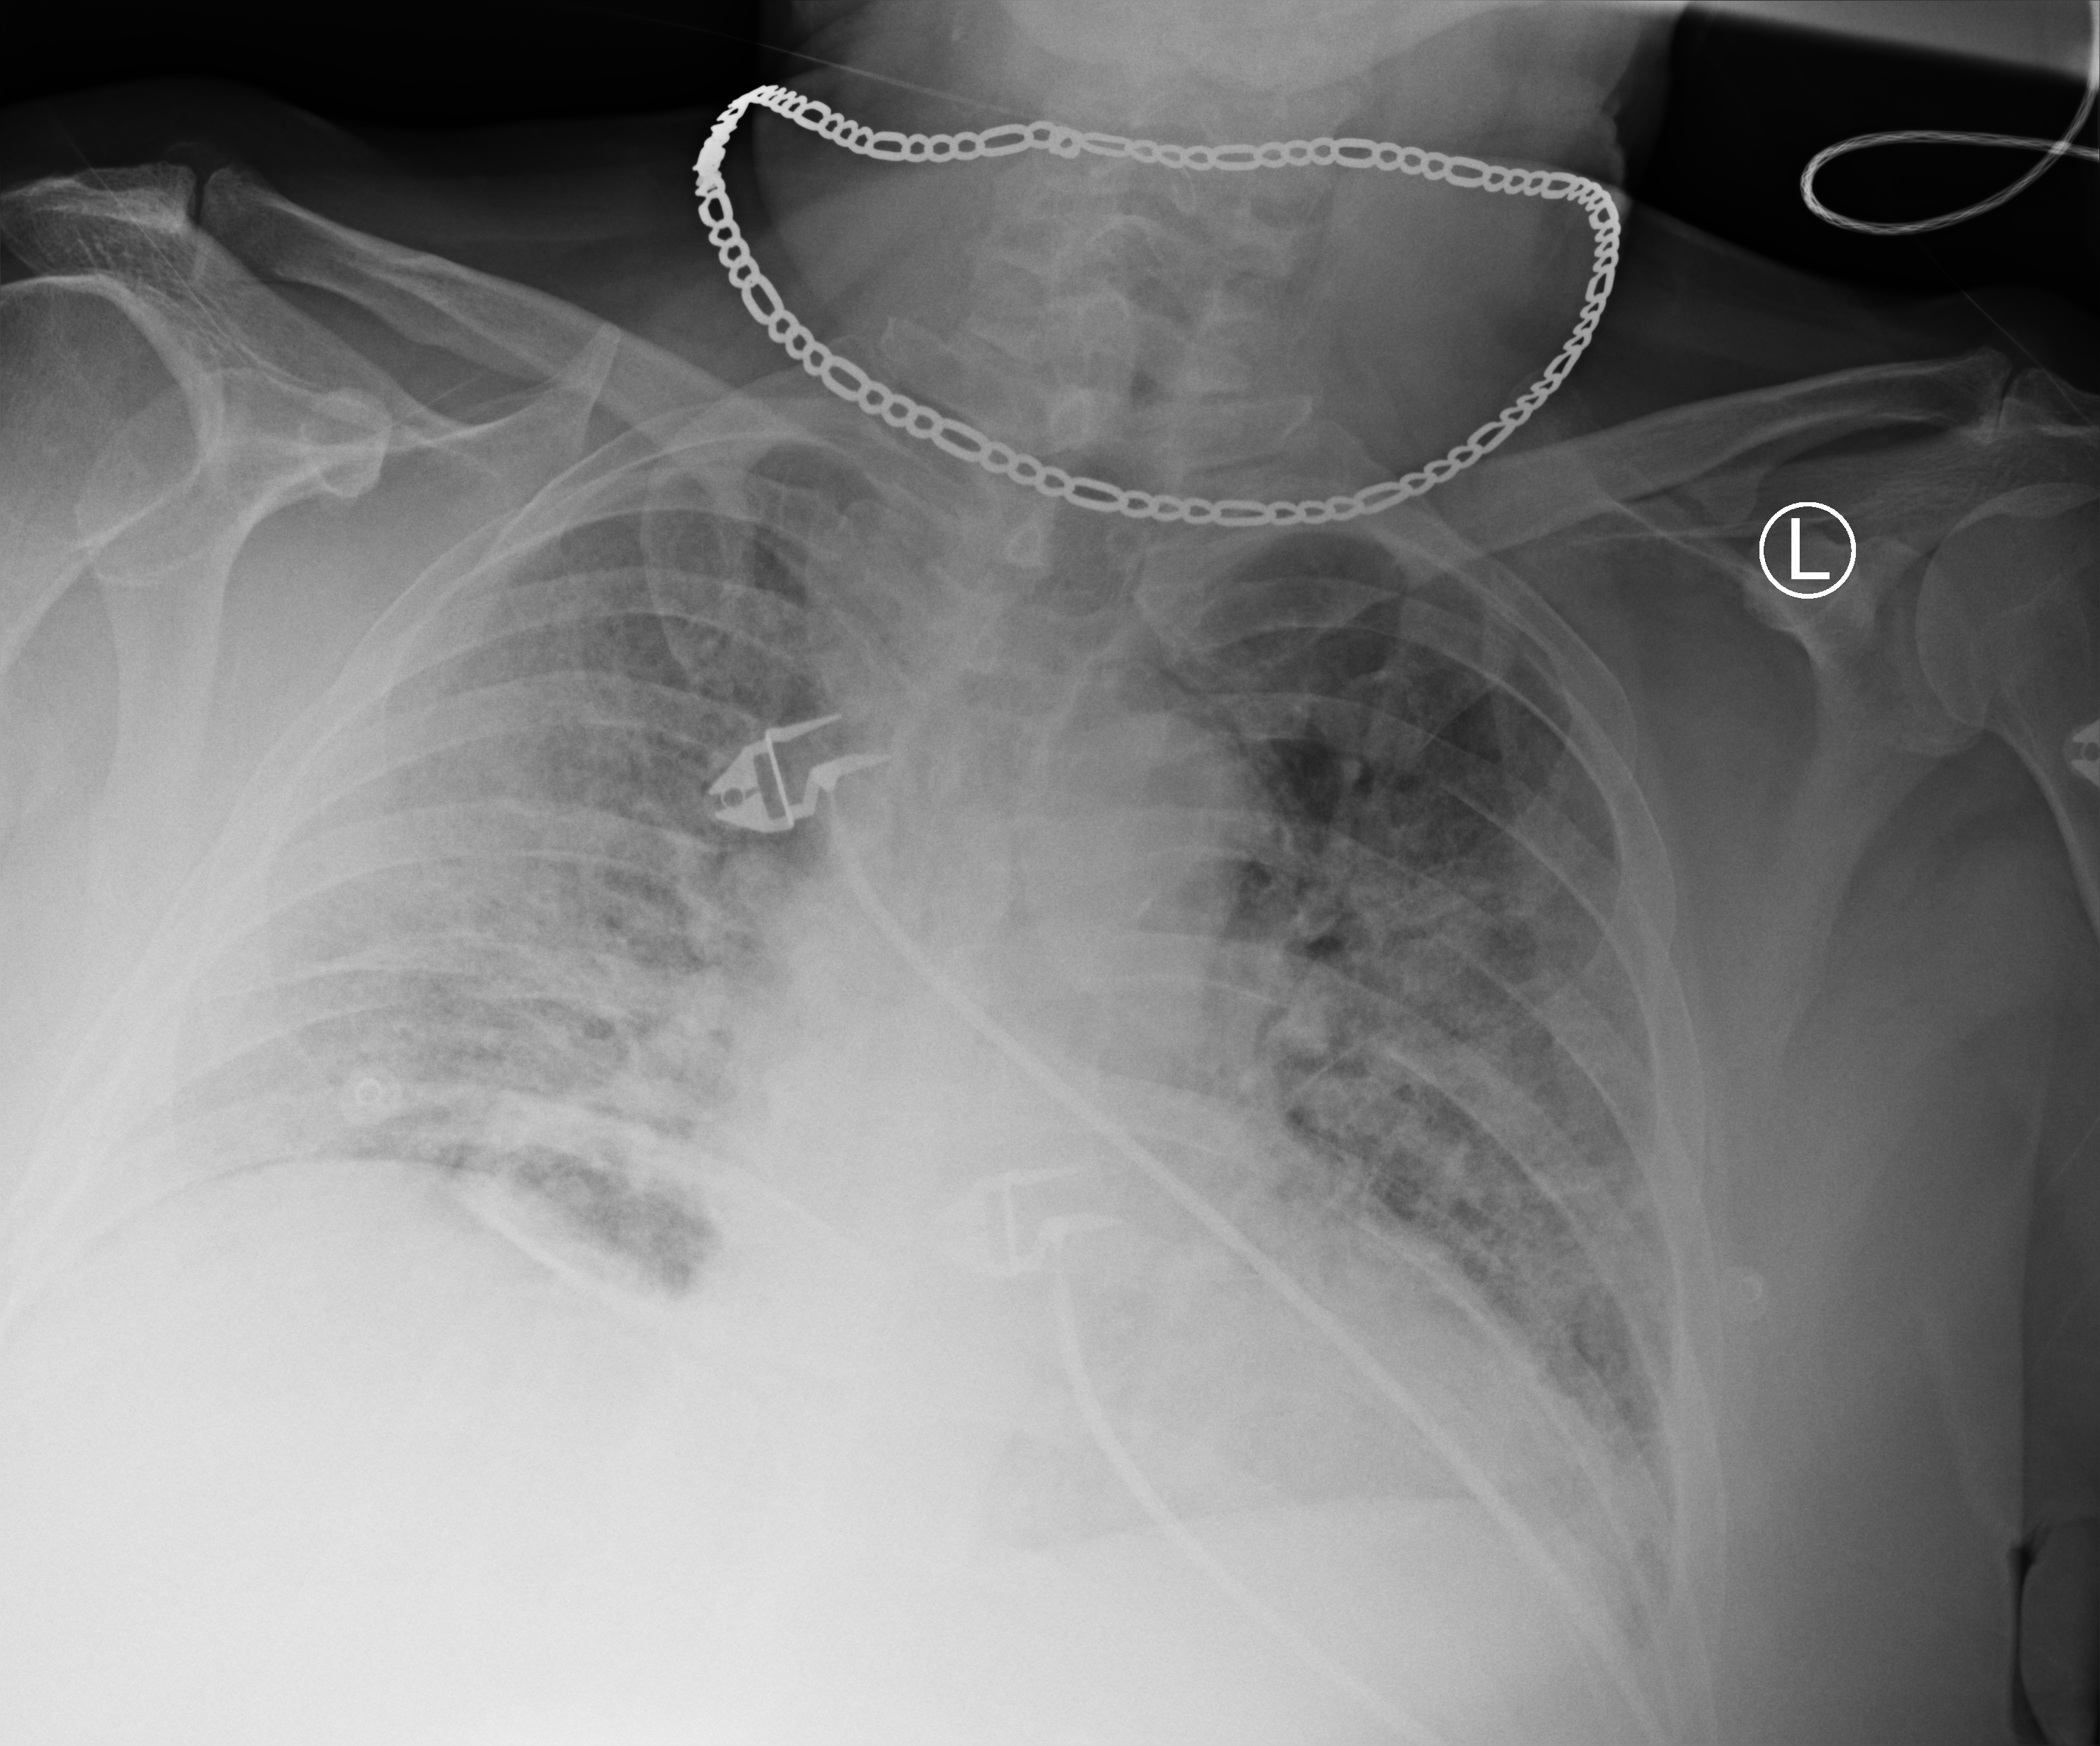
Portable chest radiograph; anteroposterior (AP) projection. Male patient hospitalised with COVID-19, age 60–74 years.
Admission-level facts for this patient (not findings on this image; timing relative to this image not recorded): mechanically ventilated during this hospital stay: no.